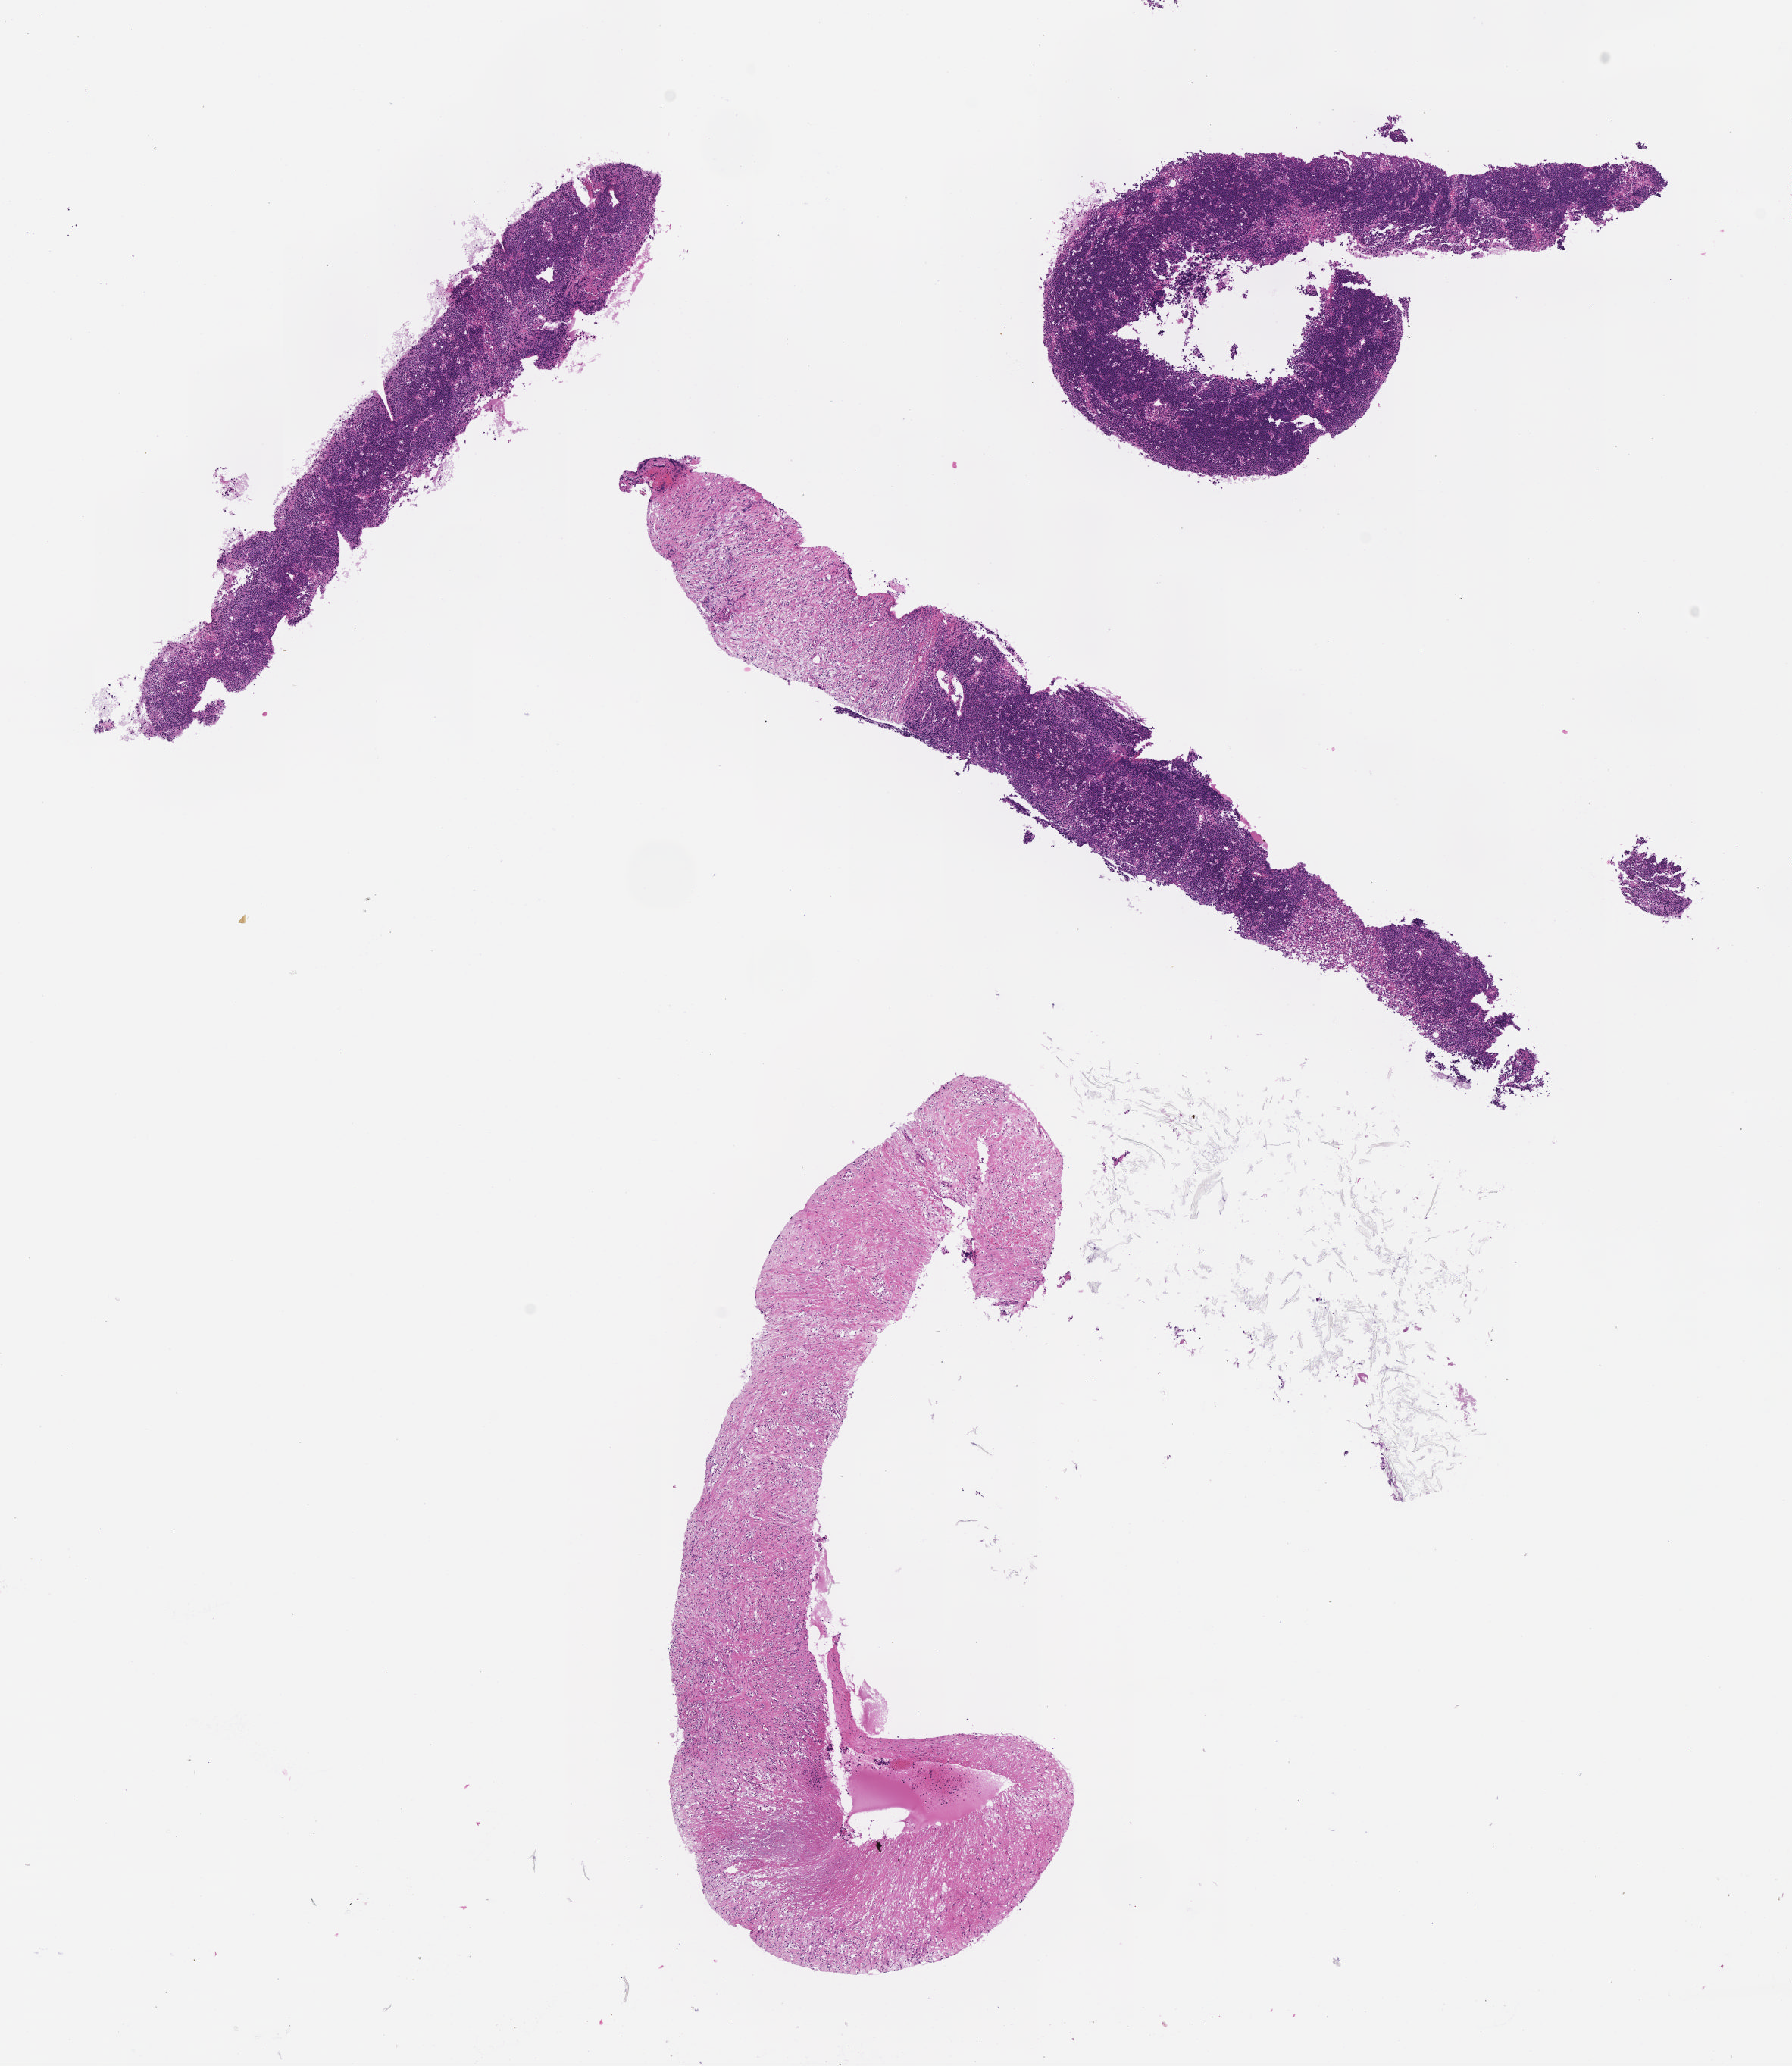
Whole-slide image, haematoxylin and eosin stain, shown as a low-resolution overview of the whole scanned area (about 9.6 x 11.0 mm). Male patient.
Specimen: tumor tissue.